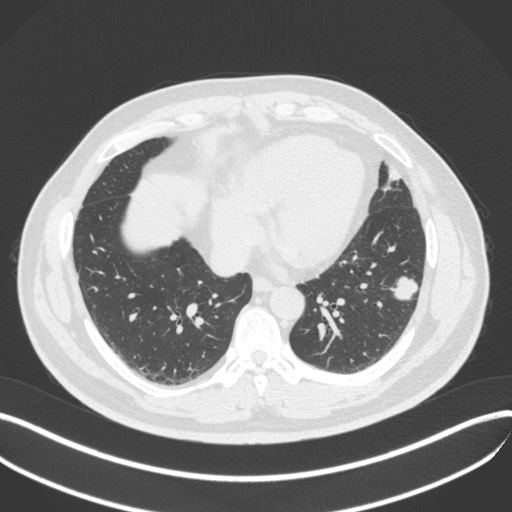
Chest CT, one axial slice. Position 149 of 420 along the scan axis. Reconstruction kernel B31f. Lung window (W 1500 / L -600 HU). 512 × 512 image matrix, field of view 400 × 400 mm. Patient: male, 39 years. Case-level facts recorded for this patient, not image findings: clinical TNM (as recorded): T2a N0 M0.
Annotated regions visible in this slice (rectangle marked by the reading radiologist):
- lung tumour (recorded histology: adenocarcinoma): bounding box [x1, y1, x2, y2] px = [387, 268, 423, 303]